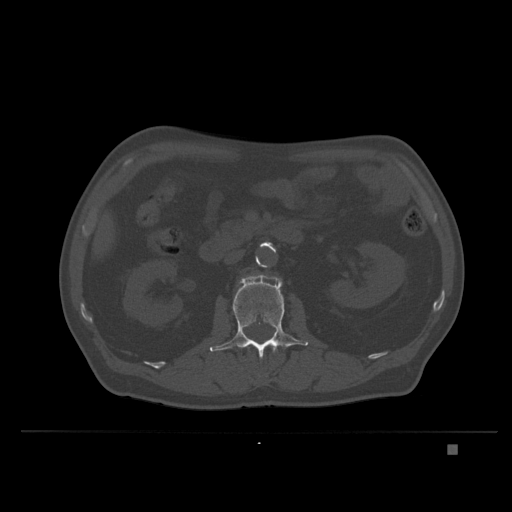
CT including the spine, one axial slice; slice 119 of 435 in the series (ordered by position); bone window (W 1800 / L 400 HU); 512 × 512 image matrix, field of view 434 × 434 mm. Male patient, age 73 years. From the clinical record (not read from this slice): primary cancer: skin.
Outlined on this slice (semi-automatically segmented with operator editing):
- L1 vertebra: bounding box <247,343,276,353> (left, top, right, bottom; pixels)
- L2 vertebra: <209,276,308,359>